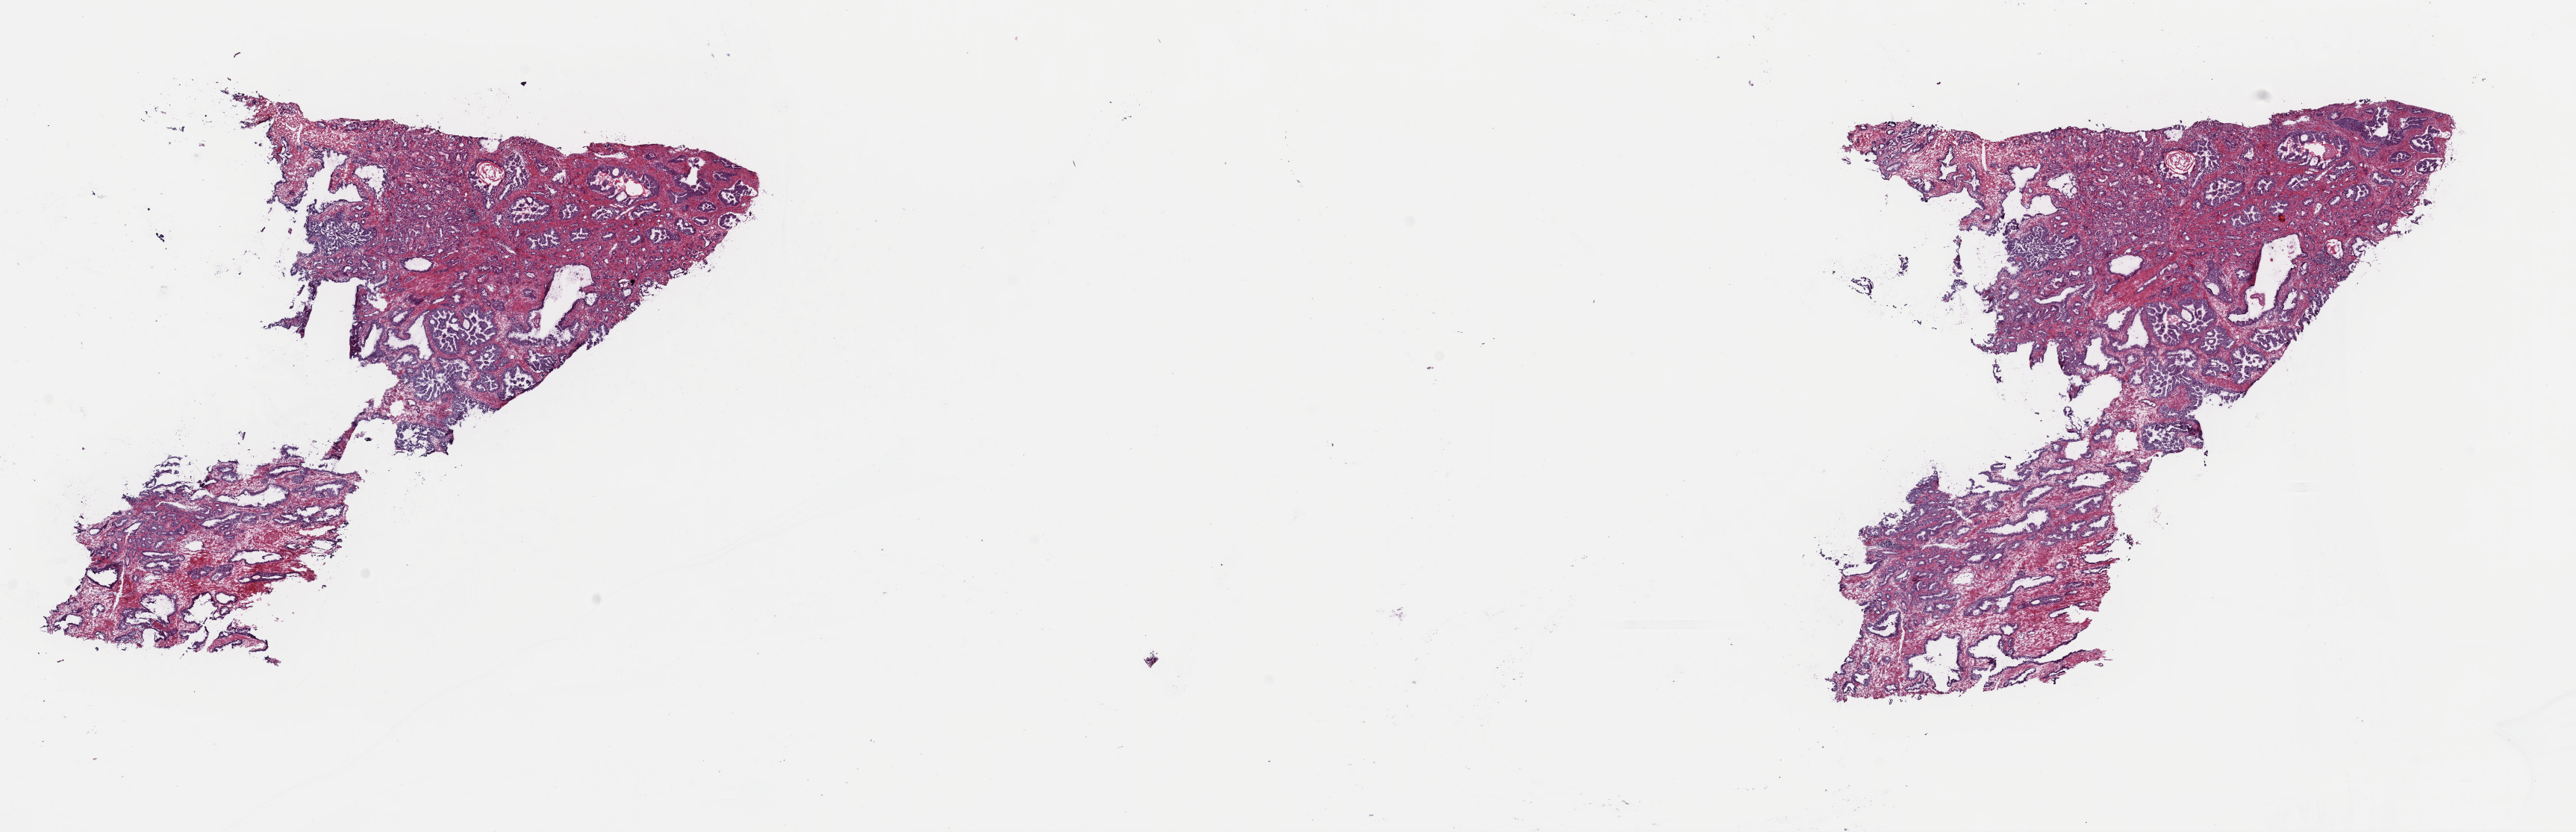
Whole-slide histology image, H&E — whole scanned area (about 27.3 x 8.8 mm) shown as a low-resolution overview. Frozen section from the top of the tissue portion. Sample: primary tumour, prostate. Male patient; age at initial diagnosis 63 years. Gleason score: 7 (3+4). Composition of this section per pathologist review: tumour cells 70%, tumour nuclei 75%, normal cells 30%, stromal cells 0%, necrosis 0%. Infiltration values recorded for this section: lymphocyte infiltration 0%, monocyte infiltration 0%, neutrophil infiltration 0%.
- histologic diagnosis: Adenocarcinoma, NOS
- laterality: bilateral